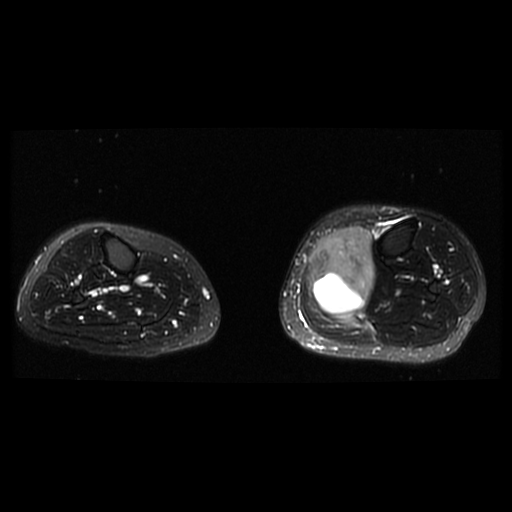
MRI of an extremity soft-tissue mass, one axial slice. Slice 13 of 38 in the series (ordered by position). T2-weighted fat-saturated. 6 mm slice thickness. 512 × 512 image matrix, field of view 330 × 330 mm. Female patient. Case-level facts recorded for this patient, not image findings: histological type: extraskeletal high grade osteogenic sarcoma; grade: high; site of the primary tumour: left calf.
Outlined on this slice (manually delineated by an expert):
- gross tumour volume (mass): box from (x=309, y=226) to (x=375, y=315) px